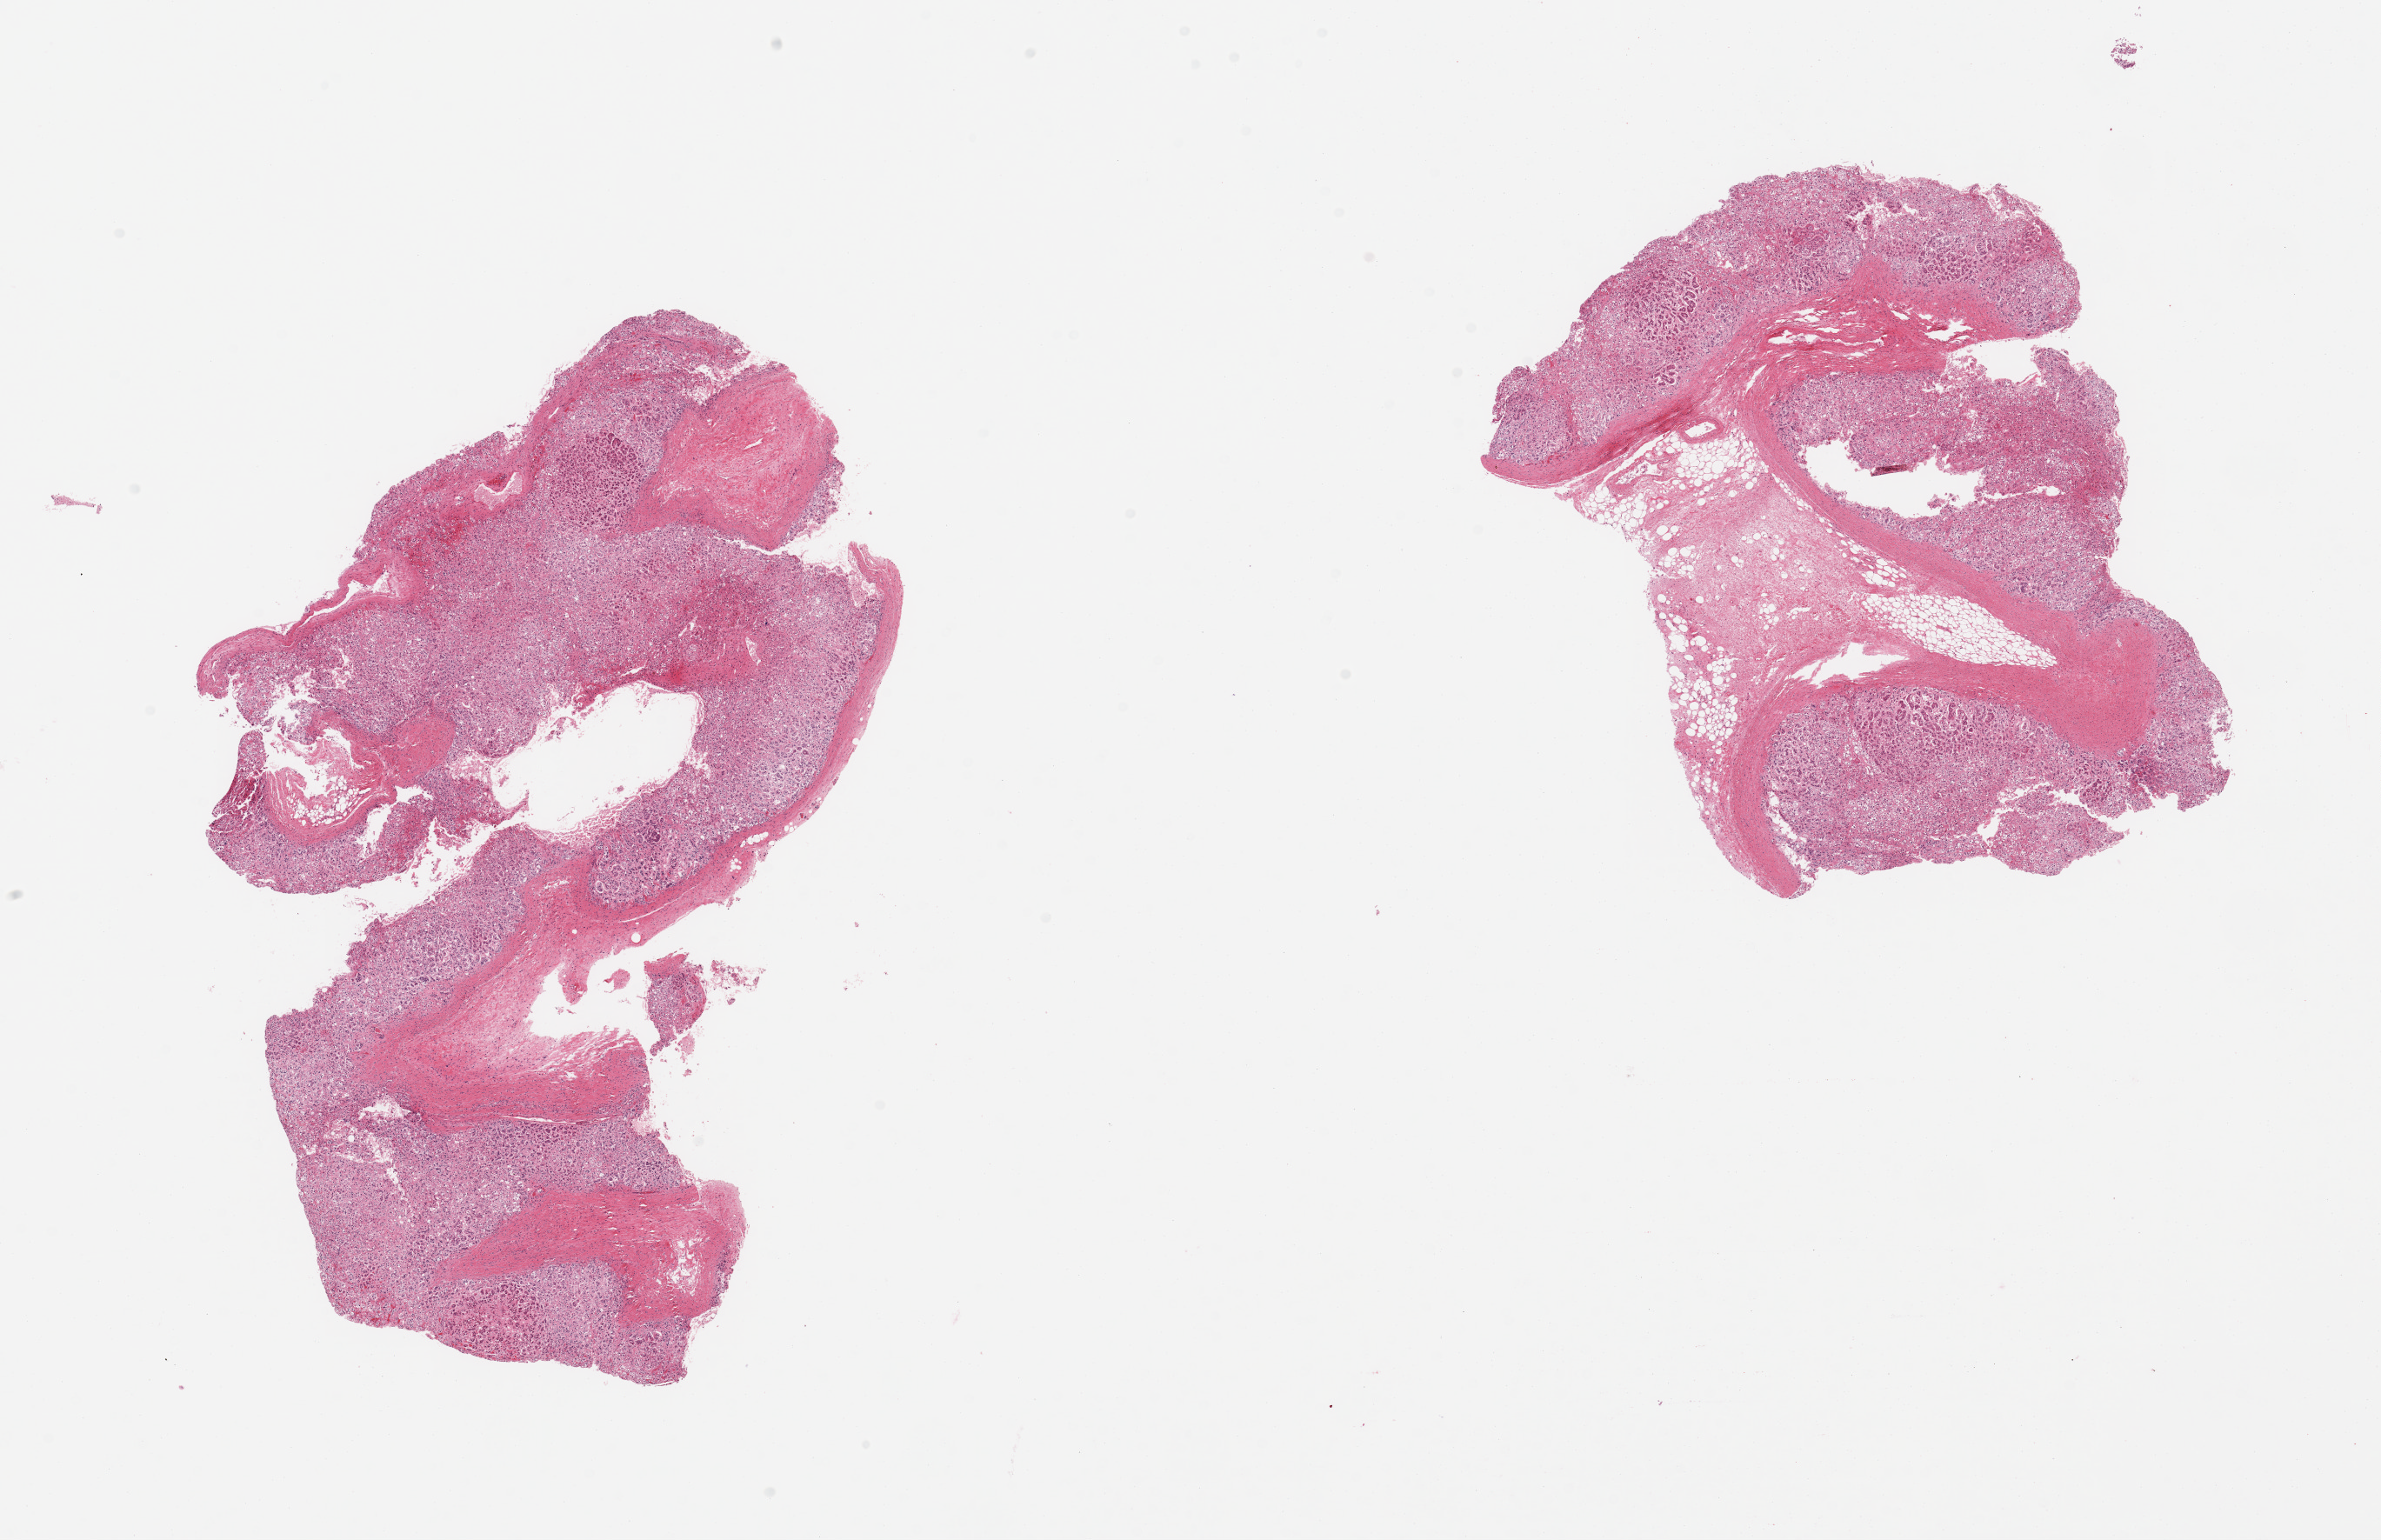
Haematoxylin and eosin whole-slide image, low-resolution overview of the scanned area, about 21.7 x 14.0 mm (slide scanned at 20x). PAXgene-fixed, paraffin-embedded tissue. Target tissue: adrenal gland. Tissue donor sample. Donor sex: male.
- pathologist's review note for this sample: 2 pieces, moderate to advance autolysis